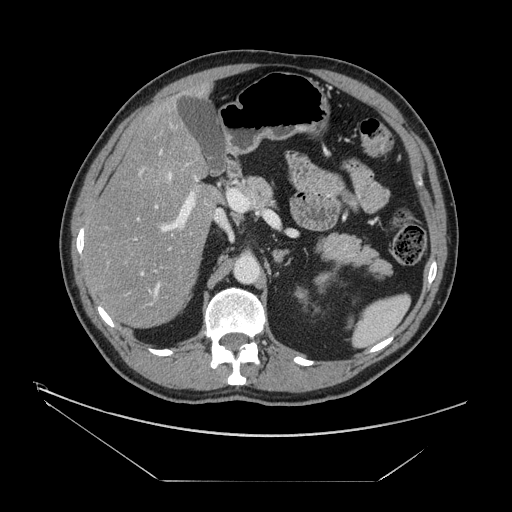
Contrast-enhanced abdominal CT, one axial slice; reconstruction kernel STANDARD; soft-tissue window (W 400 / L 40 HU); 512 × 512 image matrix. Male patient, age 65 years. Case-level facts recorded for this patient, not image findings: diagnosis: colorectal cancer liver metastases, imaged before liver resection; multiple liver metastases: yes; largest metastasis: 4.2 cm; disease in both lobes: yes.
Structures marked on this image (manually delineated by an expert):
- hepatic veins: bounding box [x1, y1, x2, y2] px = [134, 163, 189, 293]
- liver: [86, 89, 220, 328]
- planned liver remnant (the part of the liver to remain after resection): [101, 99, 216, 328]
- portal vein (with intrahepatic branches): [113, 151, 203, 325]